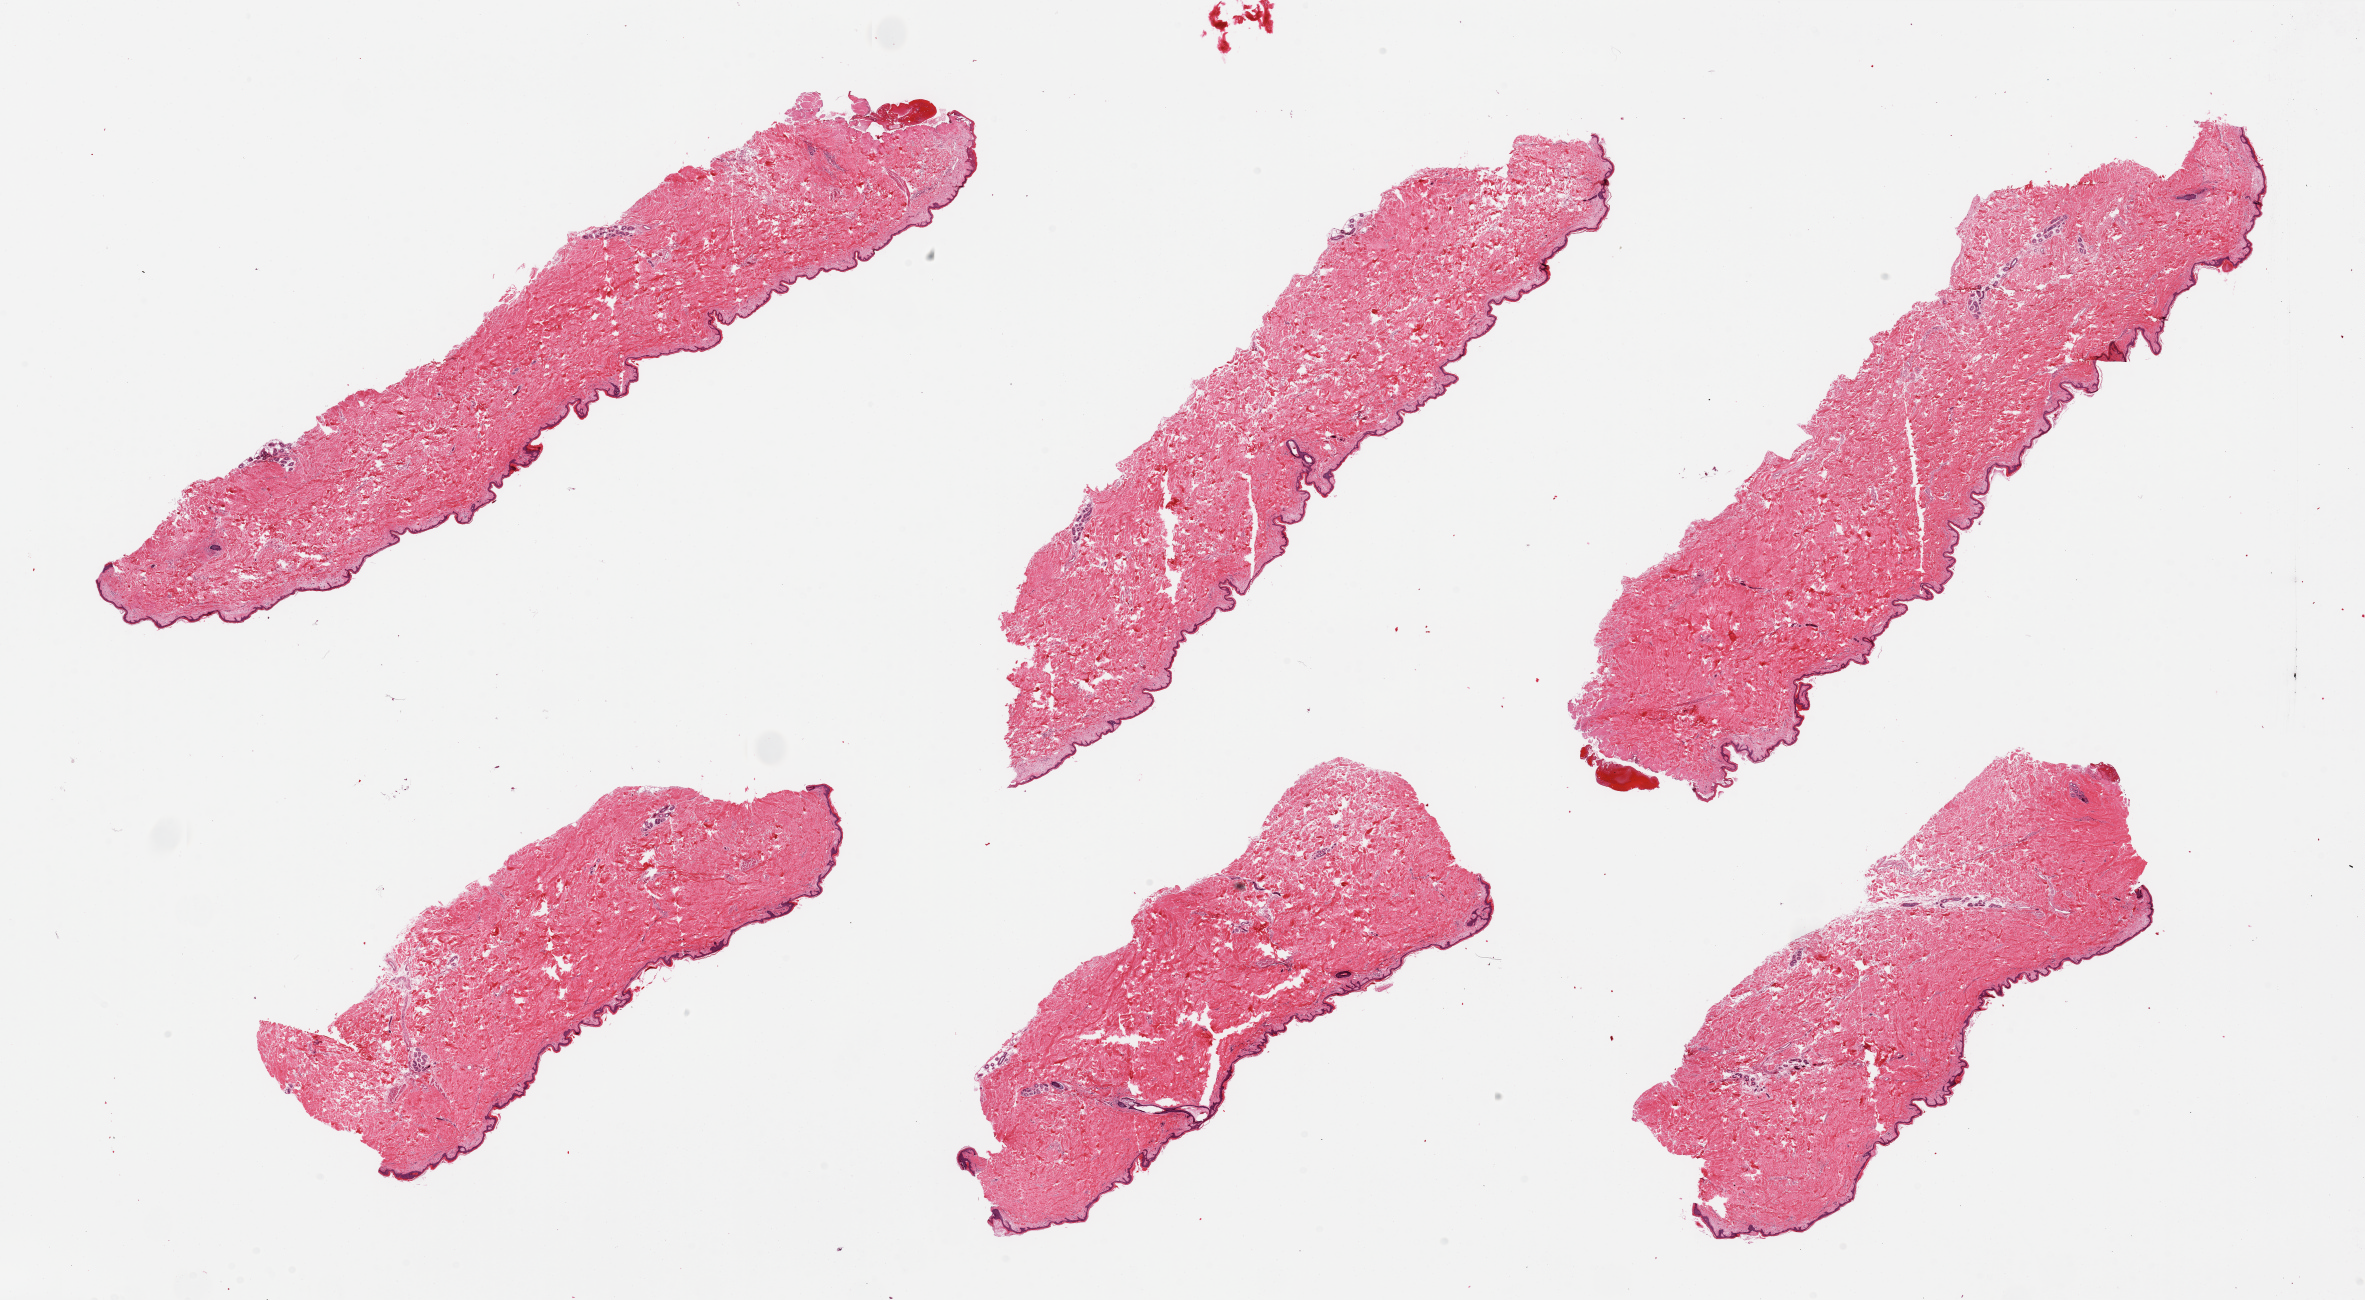
Digitized hematoxylin and eosin (H&E)-stained section, brightfield — whole scanned area (about 37.4 x 20.6 mm, acquisition: 20x scan) shown as a low-resolution overview; PAXgene-fixed, paraffin-embedded tissue; target tissue: skin of suprapubic region; tissue donor sample. Donor: male.
Reviewer comment on this tissue sample: 6 pieces well trimmed.